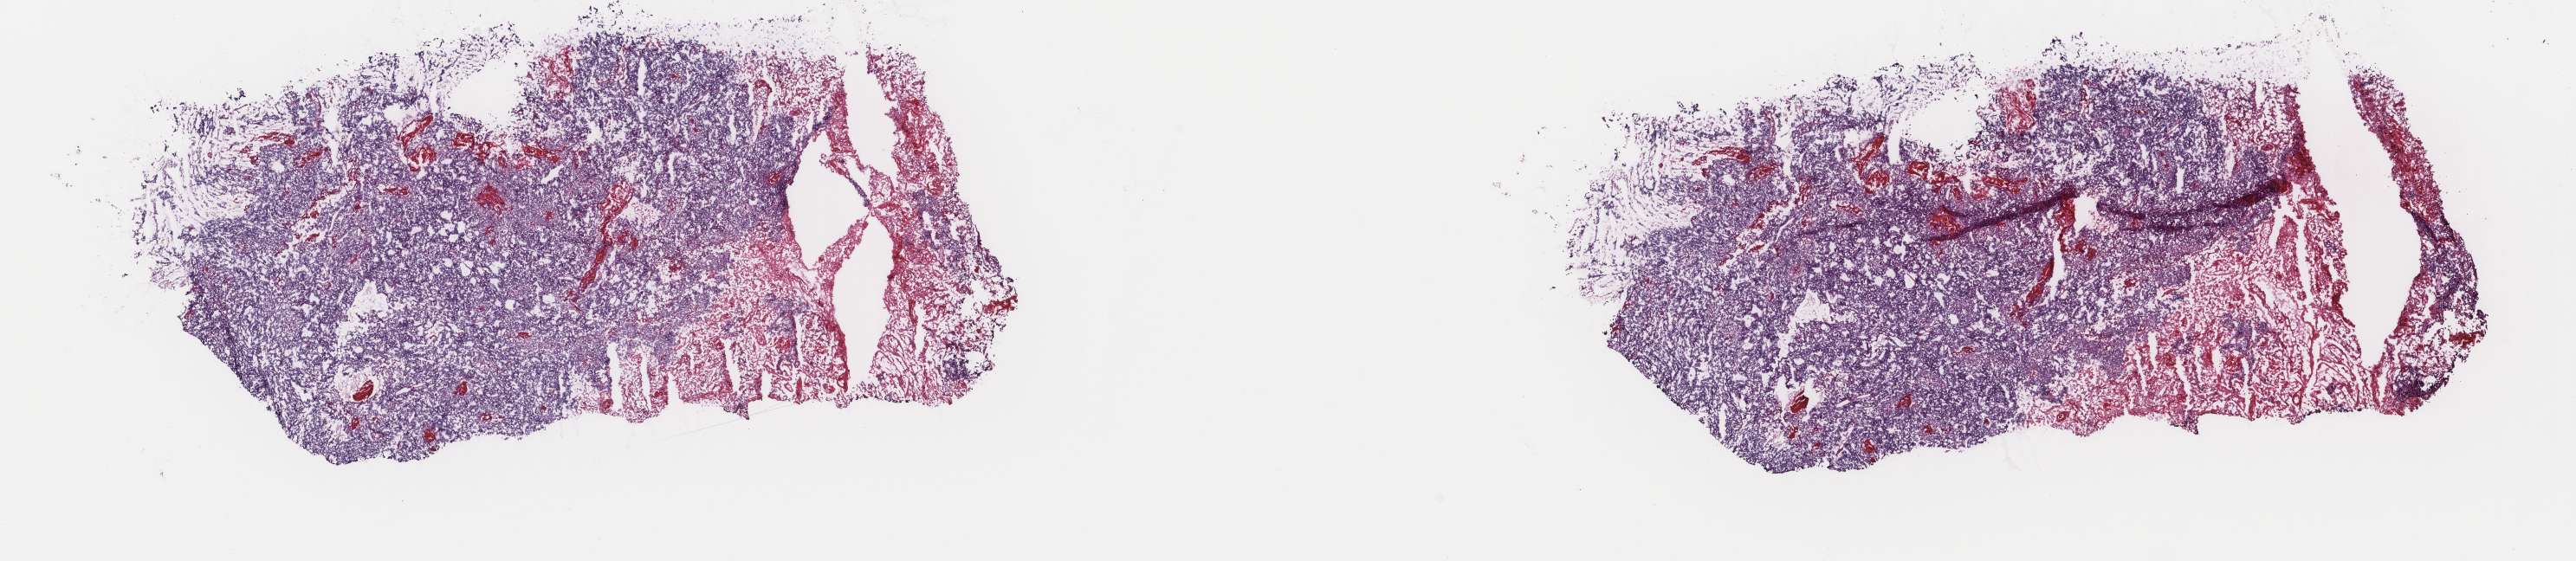
Digitized H&E-stained tissue section (whole slide) — low-resolution overview of the scanned area, about 23.6 x 5.1 mm (slide scanned at 40x); frozen section from the top of the tissue portion; sample: primary tumour, uterus. Female, age 60 years at initial diagnosis. Histologic grade: G3 (poorly differentiated). Pathologist review of this section (percent, as recorded): tumour cells 80%, tumour nuclei 96%, normal cells 0%, stromal cells 2%, necrosis 18%. Inflammatory infiltration, as recorded: lymphocyte infiltration 1%, monocyte infiltration 0%, neutrophil infiltration 0%.
Diagnosis: Endometrioid adenocarcinoma, NOS (endometrium). FIGO stage: IA.